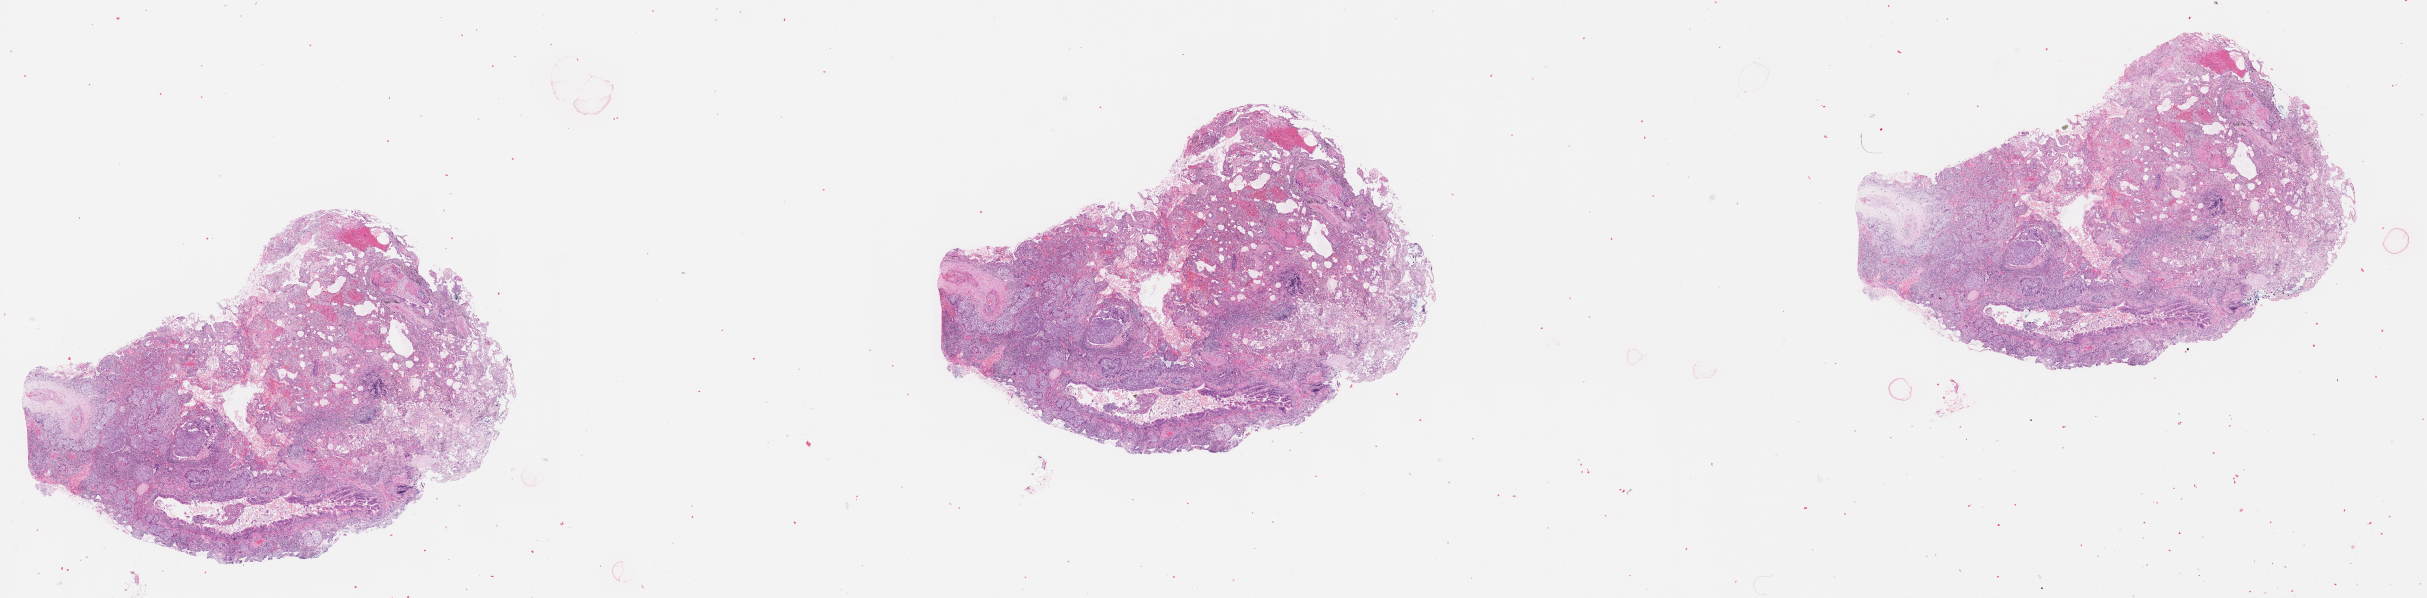
Whole-slide histology image, Hematoxylin and eosin (H&E) stained, whole scanned area (about 39.1 x 9.6 mm) shown as a low-resolution overview. Tumour tissue sample, lung. Male, 57 y/o.
Patient diagnosis (cohort enrolment): squamous cell carcinoma (lung).